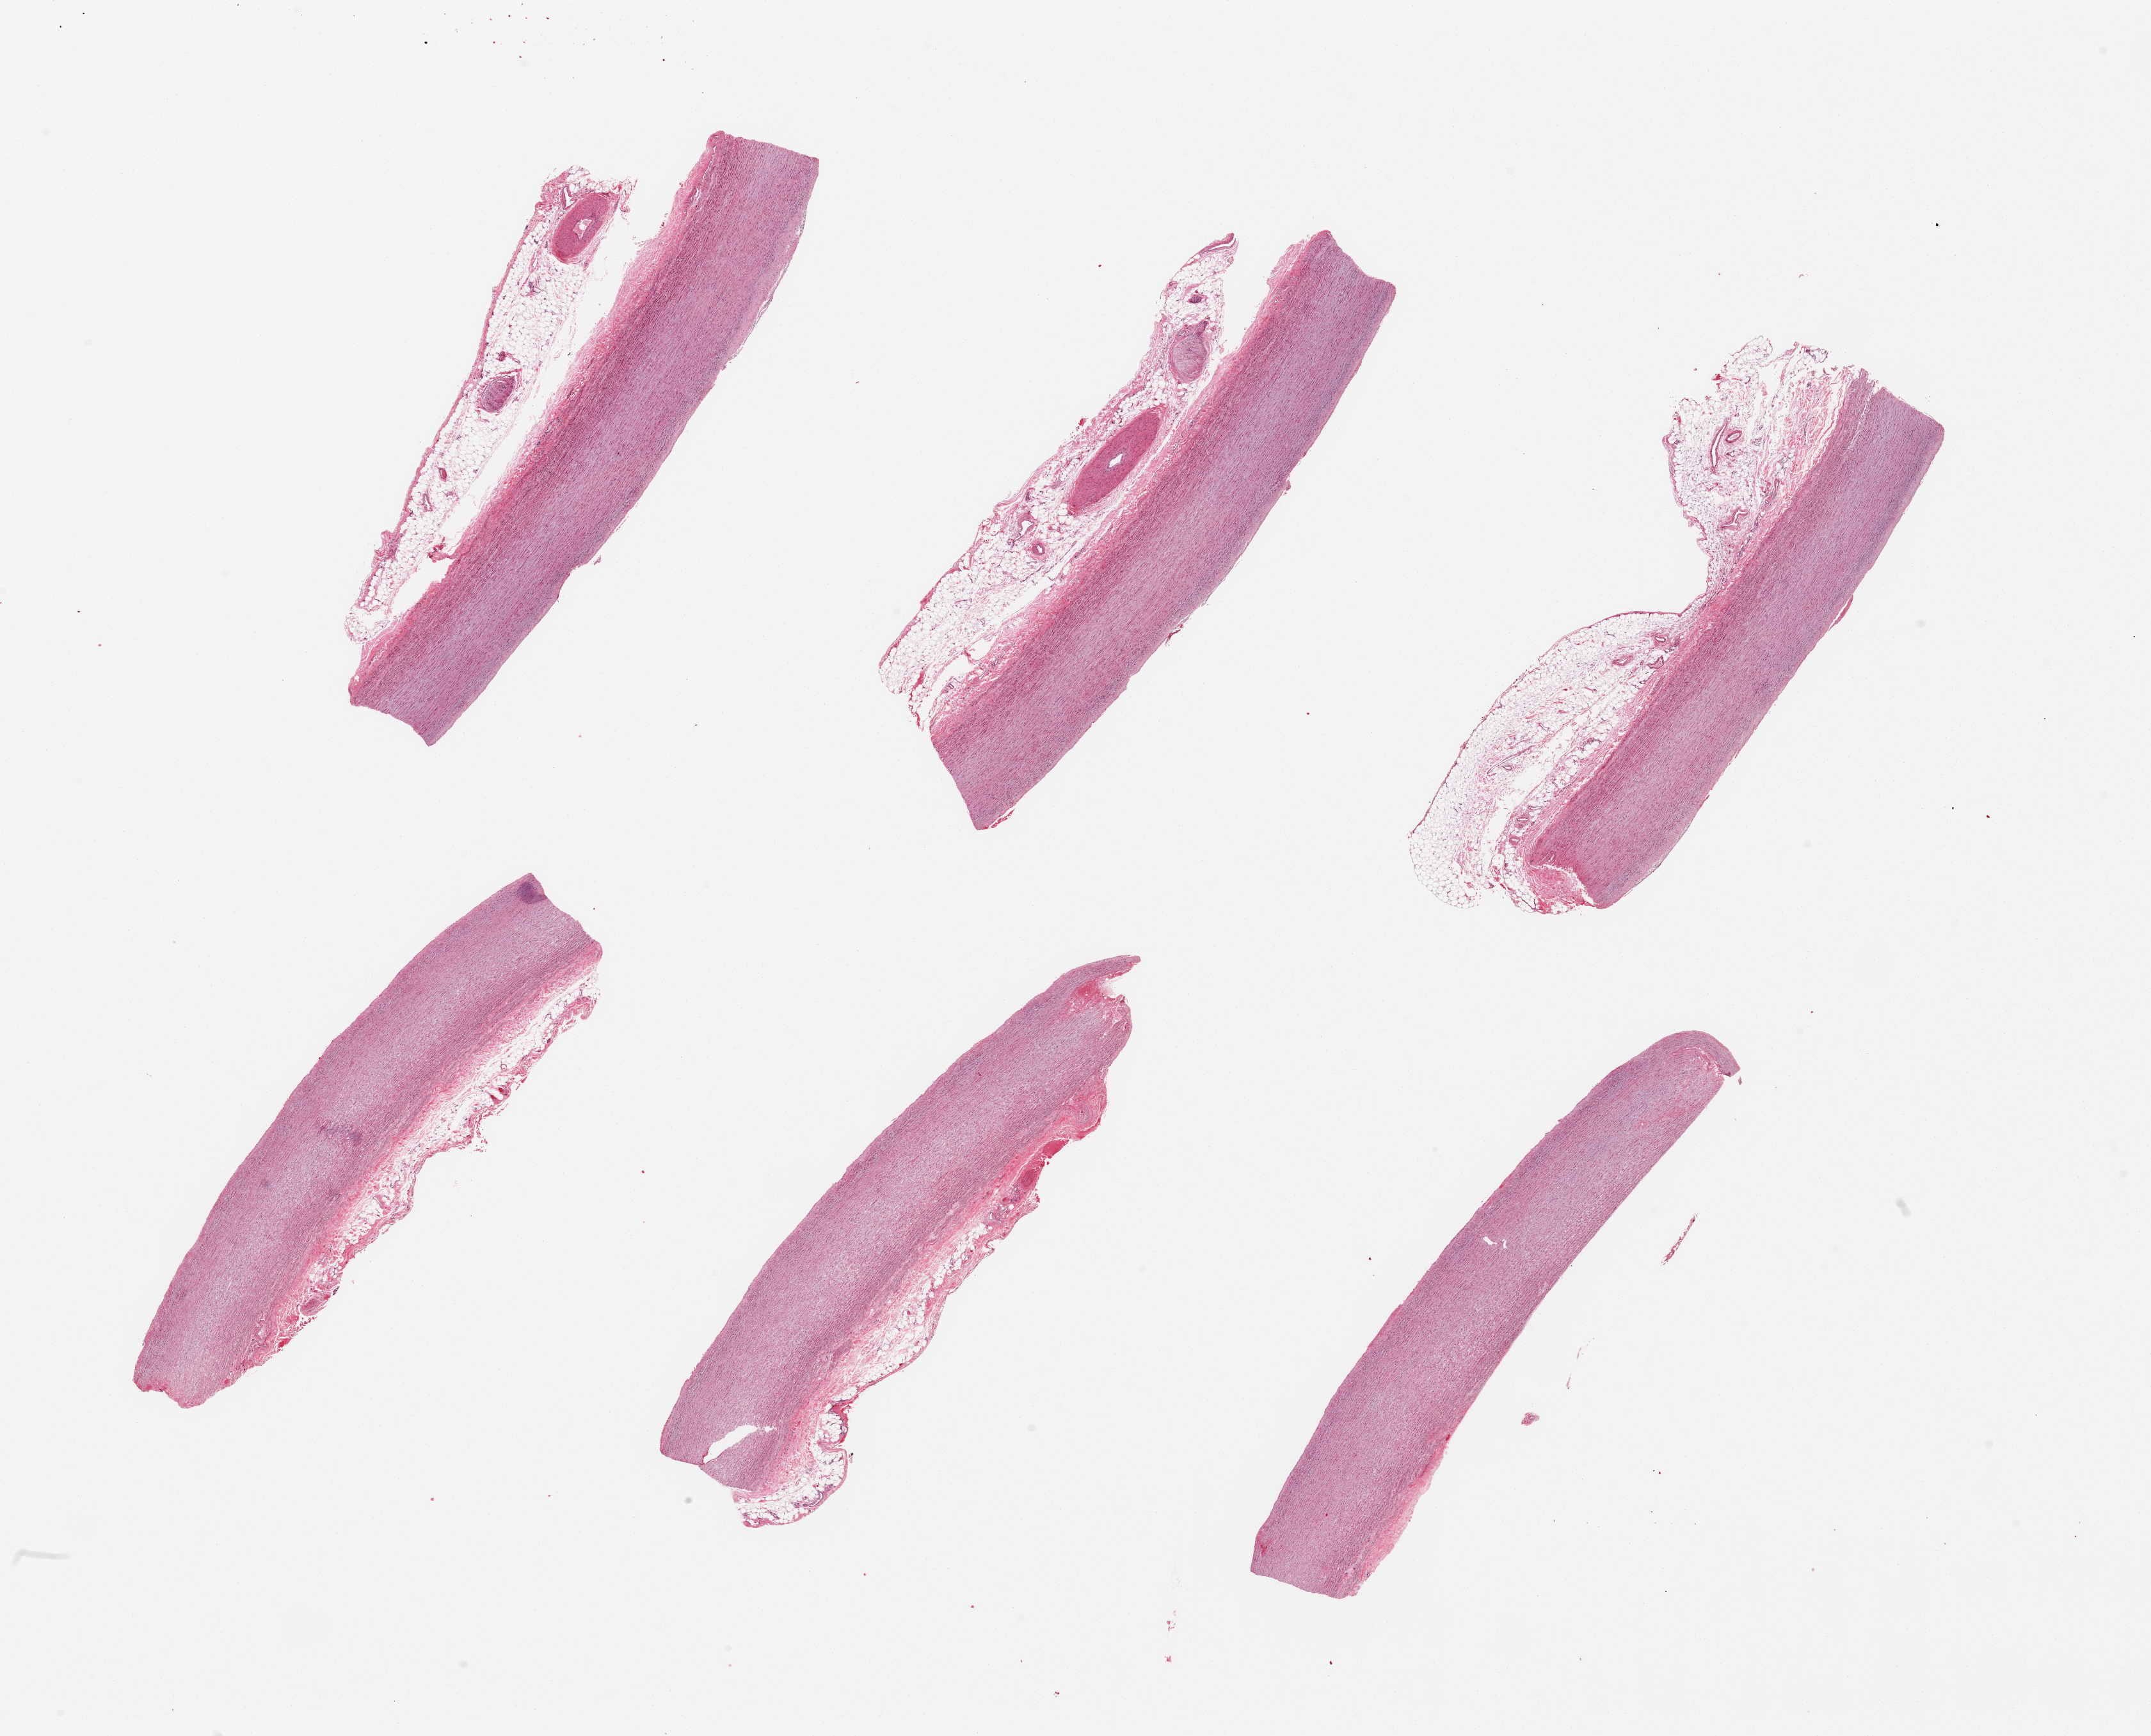
Digitized hematoxylin and eosin (H&E)-stained section, brightfield, shown as a low-resolution overview of the whole scanned area (about 26.6 x 21.5 mm), PAXgene-fixed paraffin-embedded (PFPE) section, section of aorta (target tissue), tissue donor sample. Donor sex: female.
Reviewer comment on this tissue sample: 6 pieces, adherent fat/serosa up to ~1mm.